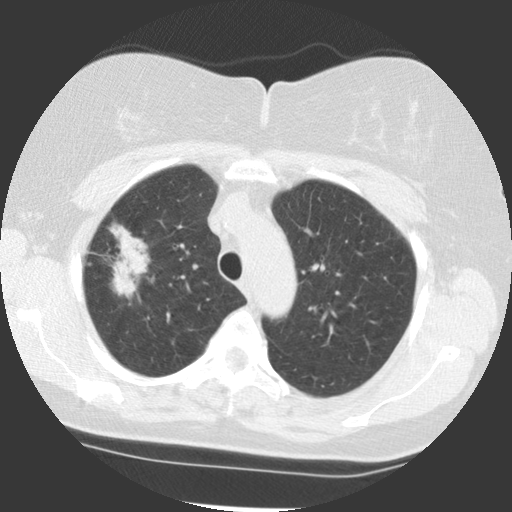
Axial slice from a low-dose chest CT screening exam, first (baseline) screen, lung window (W 1500 / L -600 HU), 512 × 512 image matrix. Female participant, aged 68 years at enrolment. Former smoker at enrolment.
Expert reader's lesion annotation, box from (x=89, y=239) to (x=152, y=297) px. The exam's reader record, not a measurement of the box and not confirmed to be the same lesion: non-calcified nodule or mass ≥4 mm, right upper lobe, 42 × 20 mm, spiculated (stellate) margins, soft tissue attenuation. Official screen result: positive, change unspecified: nodule(s) >= 4 mm or enlarging nodule(s), mass(es), or other non-specific abnormalities suspicious for lung cancer. Later outcome: lung cancer diagnosed 51 days after this screen — adenocarcinoma, NOS, right upper lobe, moderately differentiated (G2), stage IB (AJCC 6th edition), 31 mm at pathology.